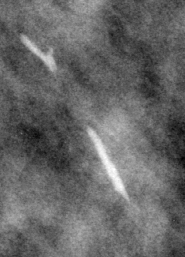
Region of interest cut from a scanned film mammogram (one marked finding), left breast, MLO view, BI-RADS breast density category 3 (scale 1–4).
- Marked abnormality: calcifications, morphology large rodlike / round and regular, distribution regional; BI-RADS assessment category 2; subtlety rating 5 on a 1 (subtle) to 5 (obvious) scale; benign without callback (not worked up further).